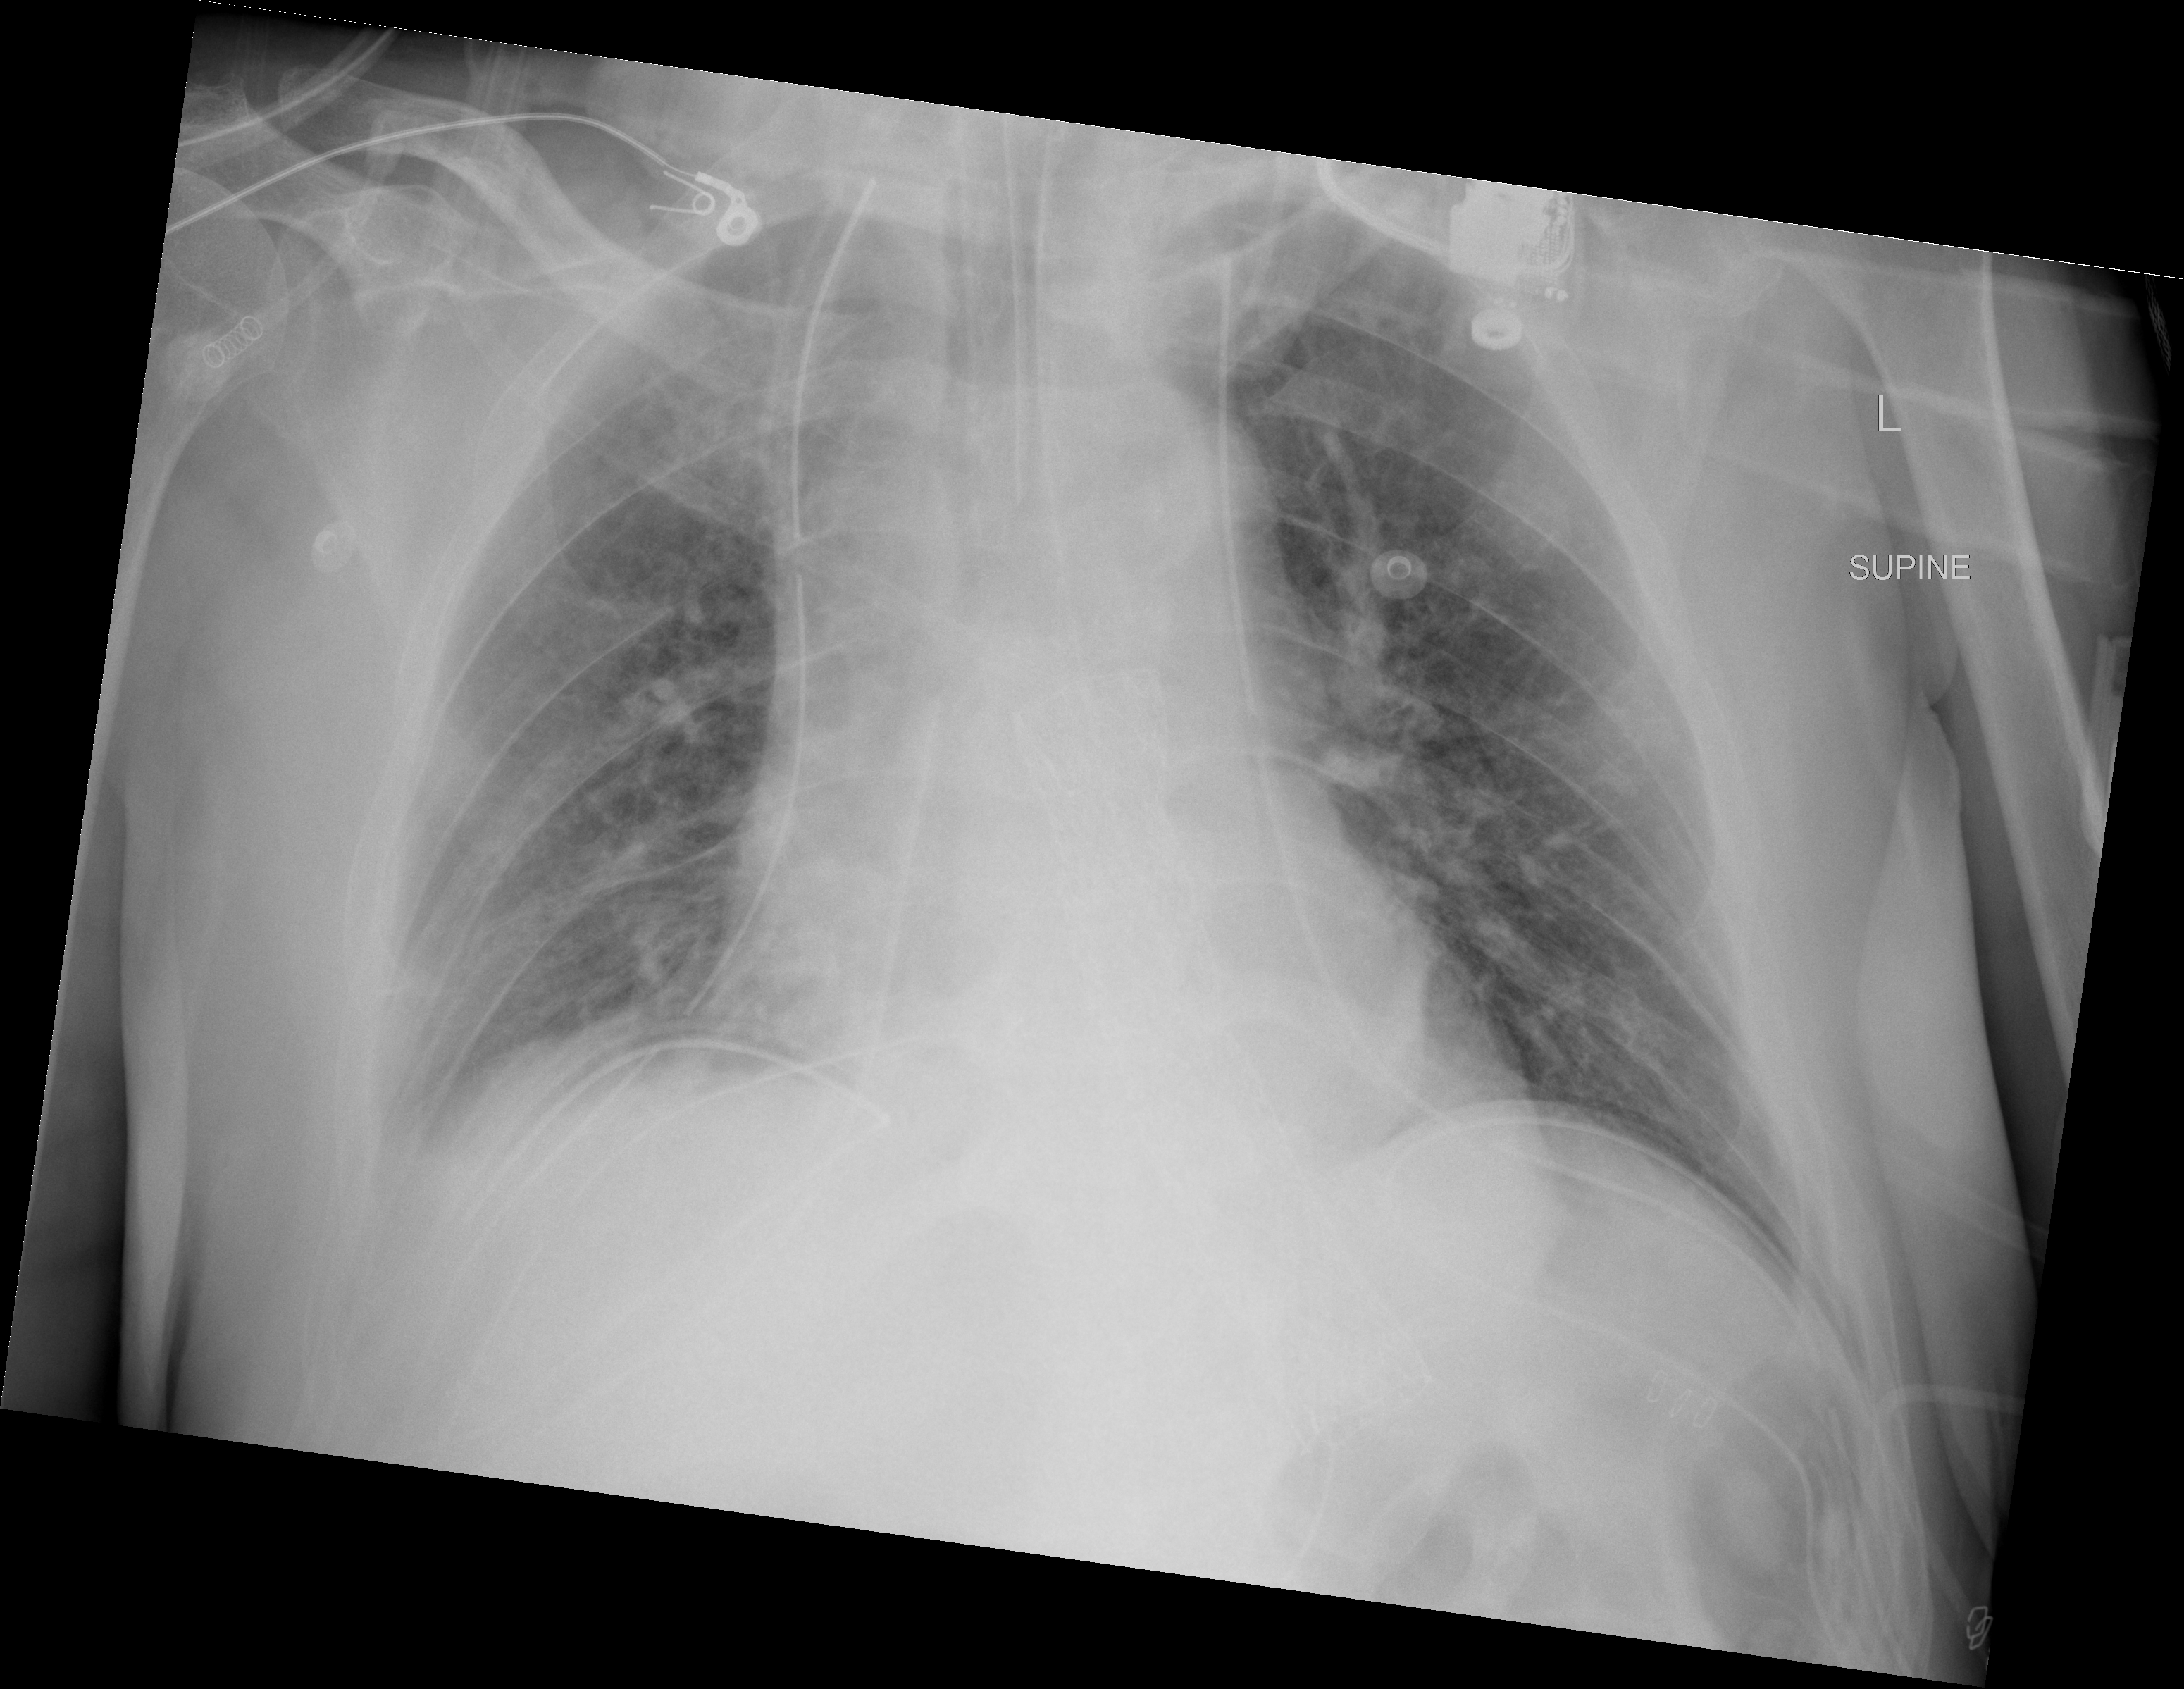
Portable chest radiograph, AP projection. Male patient, age 64 years; imaged 0 days after the COVID-19 diagnosis.
Key findings recorded by the radiologist: Atelectasis and pleural effusion on the right with no acute airspace changes on the left.